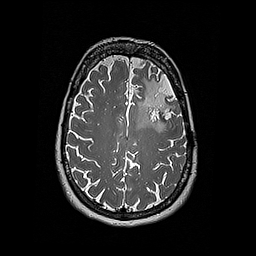
Brain MRI from a brain-tumour surgery series, one axial slice; slice 129 of 192 in the series (ordered by position); 1 mm slice thickness; 256 × 256 image matrix, field of view 250 × 250 mm. From the clinical record (not read from this slice): histopathology: Oligodendroglioma; WHO grade: 2; IDH mutation: yes; tumour location: Left Frontal.
Structures marked on this image (outlined manually by an expert reader):
- tumour: bounding box (x1, y1, x2, y2) in pixels: (134, 78, 158, 128)